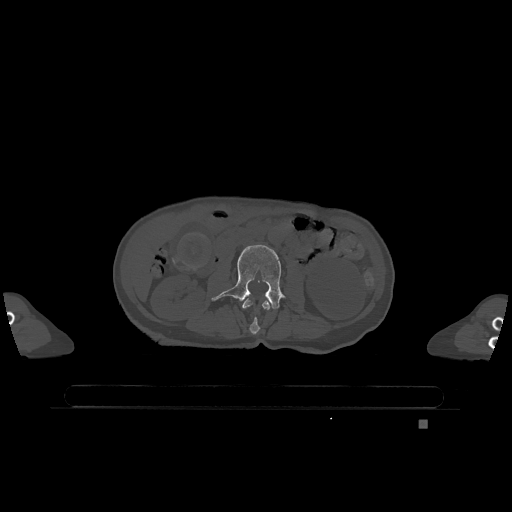
CT including the spine, one axial slice. Position 370 of 1317 along the scan axis. Bone window (W 1800 / L 400 HU). 0.5 mm slice thickness. 512 × 512 image matrix. Female patient, age 74 years. Case-level facts recorded for this patient, not image findings: primary cancer: lung; vertebrae with lytic lesions (as recorded): T1, T4, T5, T6, L4, L5.
Structures marked on this image (semi-automatically segmented with operator editing):
- L2 vertebra: bounding box [x1, y1, x2, y2] px = [242, 299, 272, 335]
- L3 vertebra: [212, 245, 284, 309]